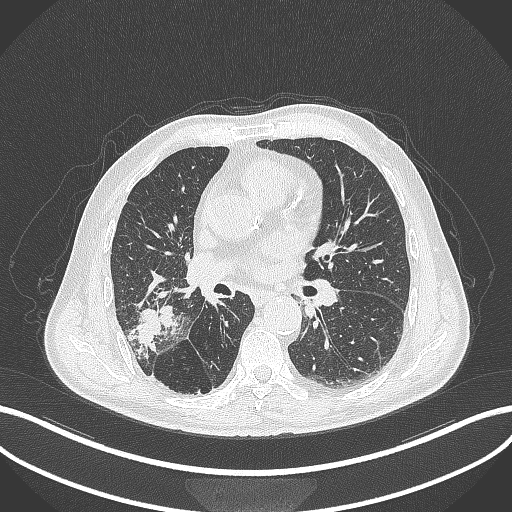
Chest CT, one axial slice. Slice 218 of 429 in the series (ordered by position). Reconstruction kernel B70f. Lung window (W 1500 / L -600 HU). 1 mm slice thickness. 512 × 512 image matrix, field of view 400 × 400 mm. Male patient, age 72 years. From the clinical record (not read from this slice): clinical TNM (as recorded): T3 N2 M0.
Structures marked on this image (bounding box drawn by a radiologist):
- lung tumour (recorded histology: adenocarcinoma): bounding box (x1, y1, x2, y2) in pixels: (128, 302, 180, 354)